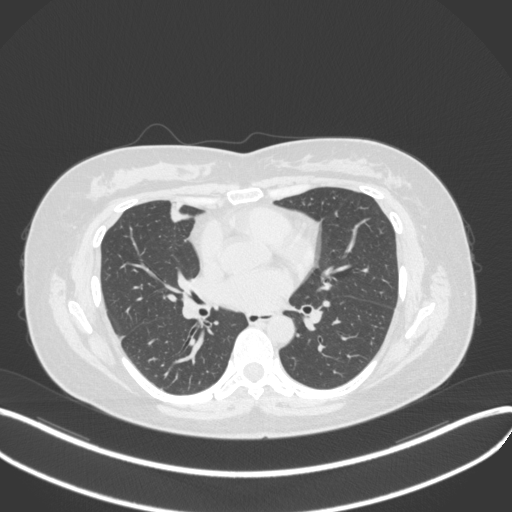
Chest CT, one axial slice; slice 157 of 272 in the series (ordered by position); reconstruction kernel B31f; lung window (W 1500 / L -600 HU); 512 × 512 image matrix. Female patient, age 42 years. From the clinical record (not read from this slice): clinical TNM (as recorded): T1b N0 M0.
Structures marked on this image (rectangle marked by the reading radiologist):
- lung tumour (recorded histology: adenocarcinoma): bounding box <166,201,194,230> (left, top, right, bottom; pixels)